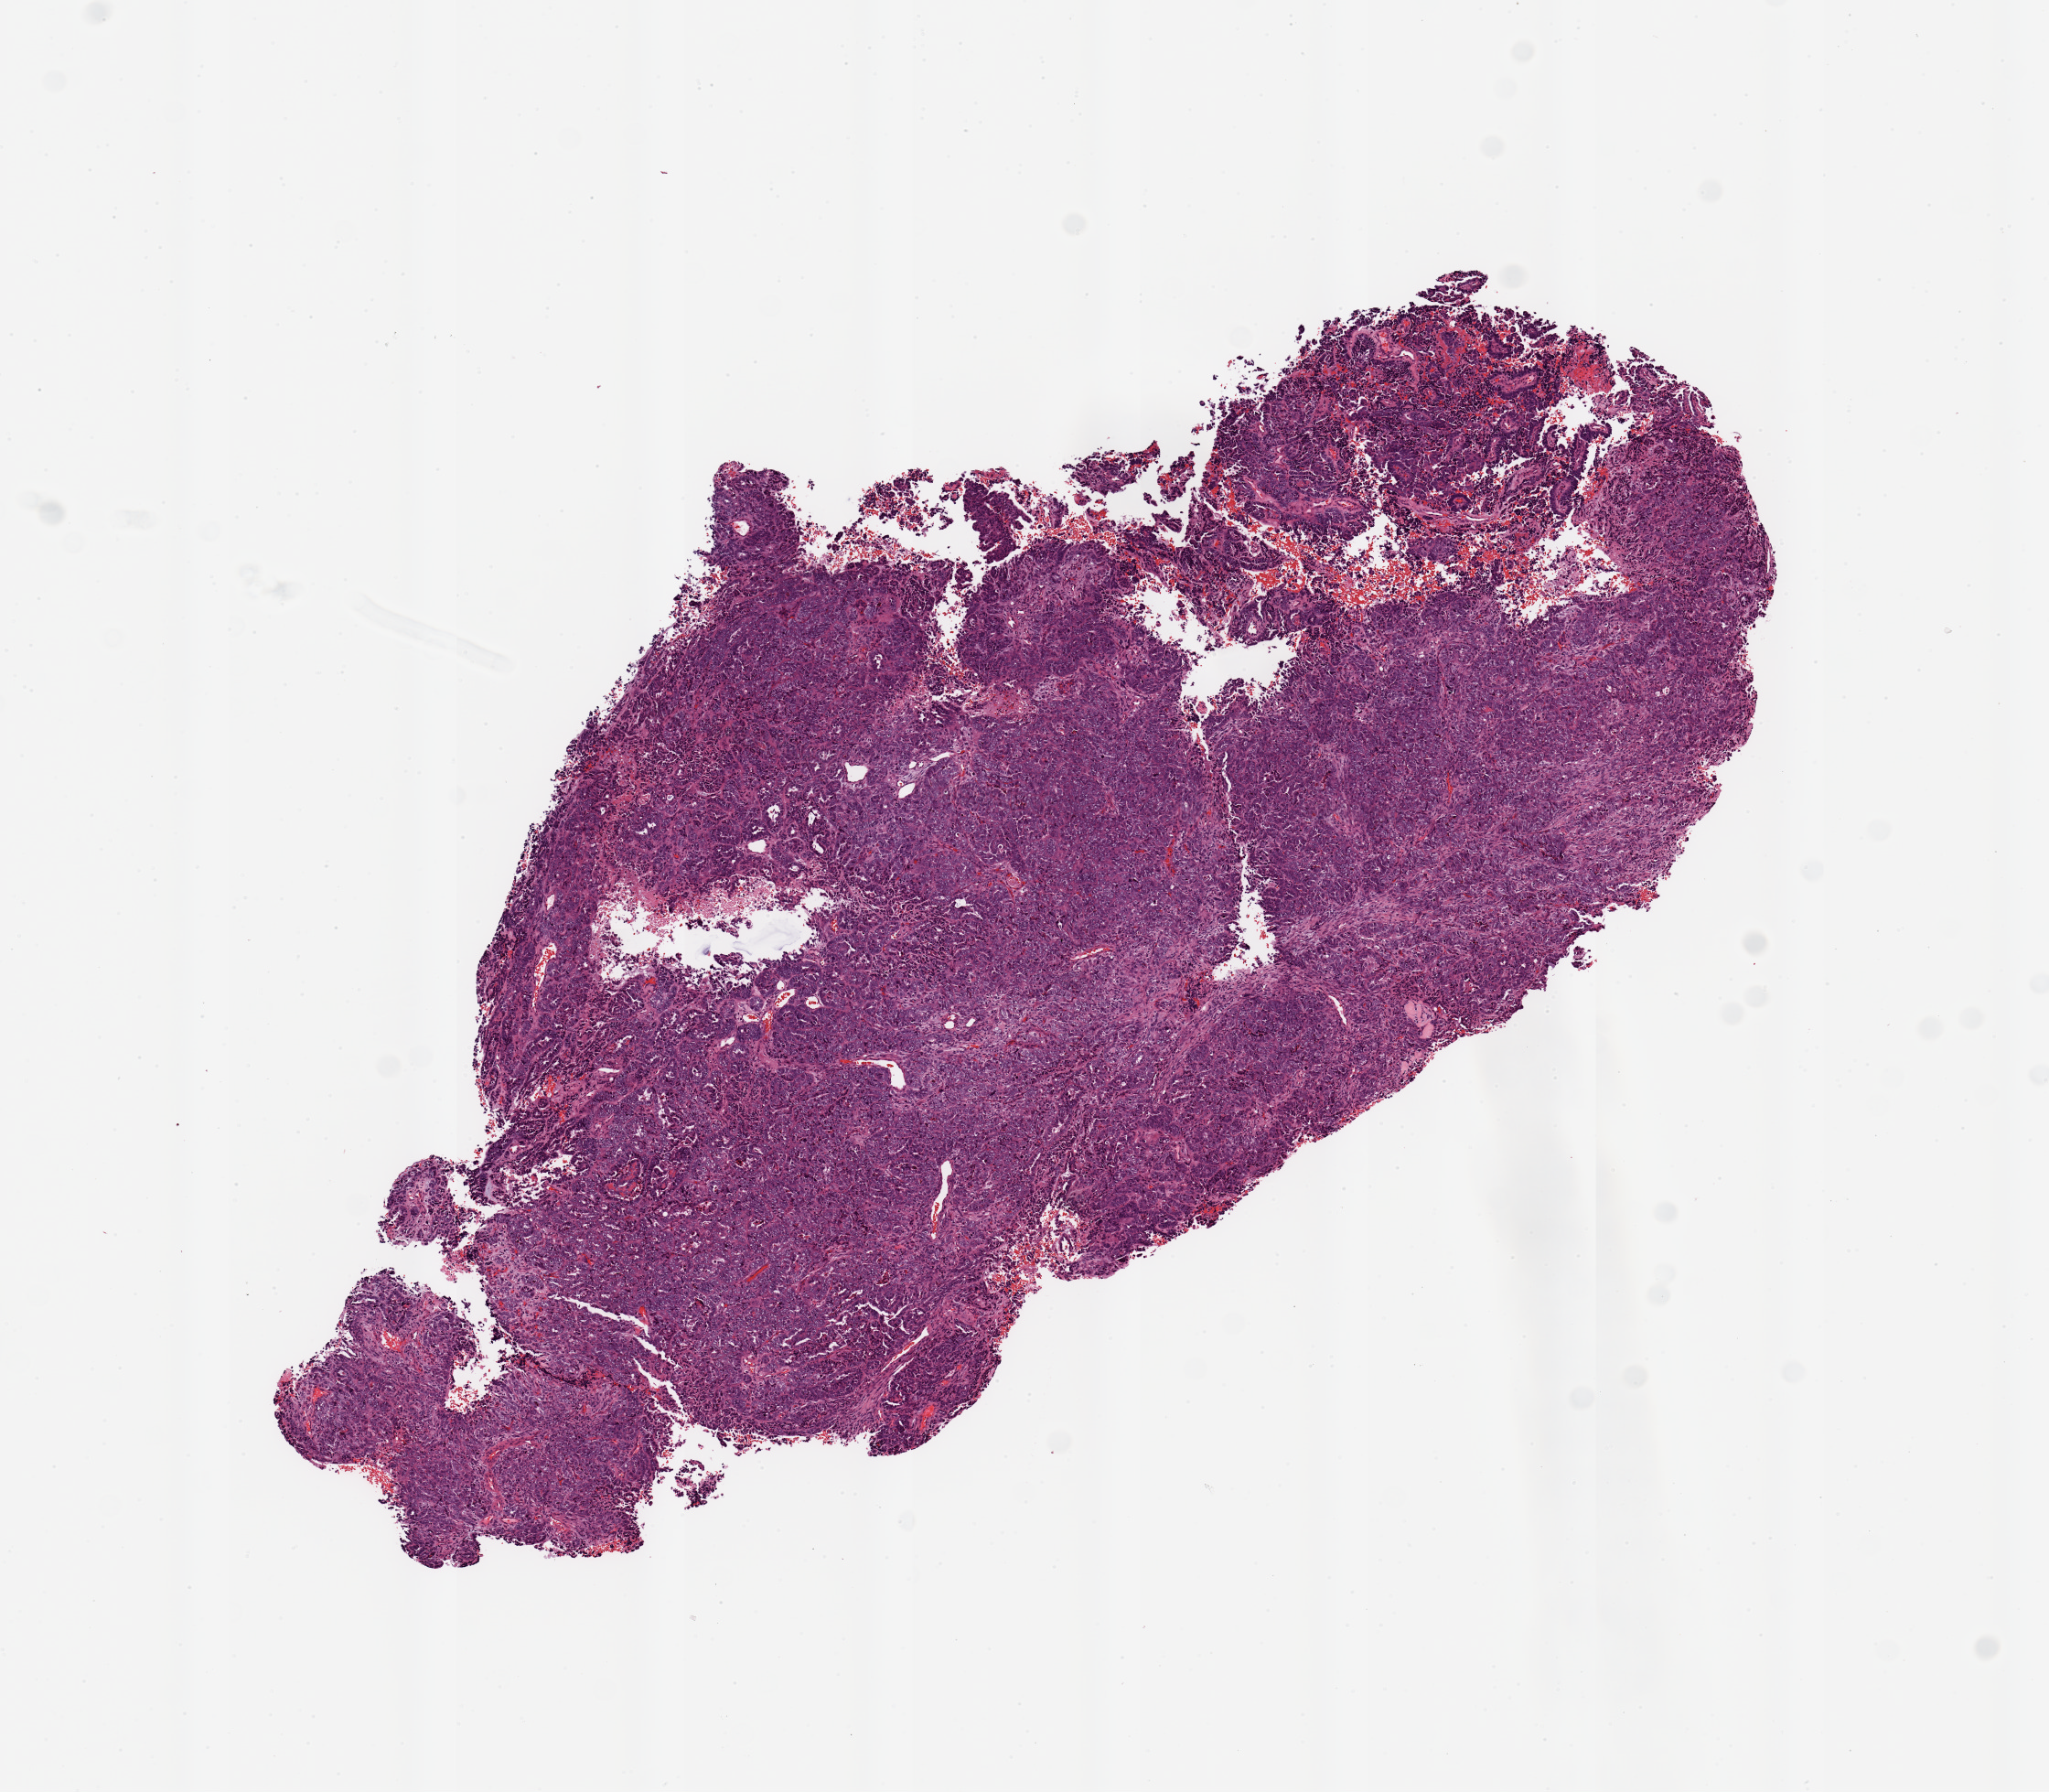
Digitized H&E-stained tissue section (whole slide), a low-resolution overview of the entire scanned area, about 8.9 x 7.7 mm (slide scanned at 20x), tumour tissue sample, sampled site: uterus. Female, 73 y/o. Histologic grade: G3 (poorly differentiated). Slide review estimates, as recorded: tumour nuclei 98%, necrosis 2%.
Histologic diagnosis: Endometrioid adenocarcinoma, NOS. AJCC pathologic stage: I.